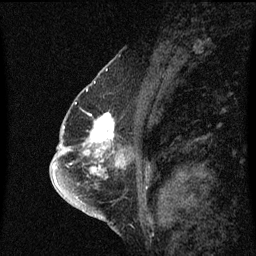
Breast MRI (dynamic contrast-enhanced), one sagittal slice. Slice 37 of 60 in the series (ordered by position). Dynamic contrast-enhanced series, image 2 of 3 at this slice position (ordered by acquisition). 1.5 T. TE 4.2 ms, TR 8.4 ms. 2 mm slice thickness. 256 × 256 image matrix. Female patient, age 57 years. Case-level facts recorded for this patient, not image findings: setting: breast cancer imaged before/during neoadjuvant chemotherapy; receptor status: HR-positive, HER2-negative.
Structures marked on this image (semi-automatically segmented with operator editing):
- analysis volume of interest (the breast-tissue region the enhancement analysis was run in; not a lesion): bounding box <87,114,116,145> (left, top, right, bottom; pixels)
- tumour enhancement mask (voxels above the 70 % enhancement threshold inside the analysis volume of interest): <90,114,115,143>